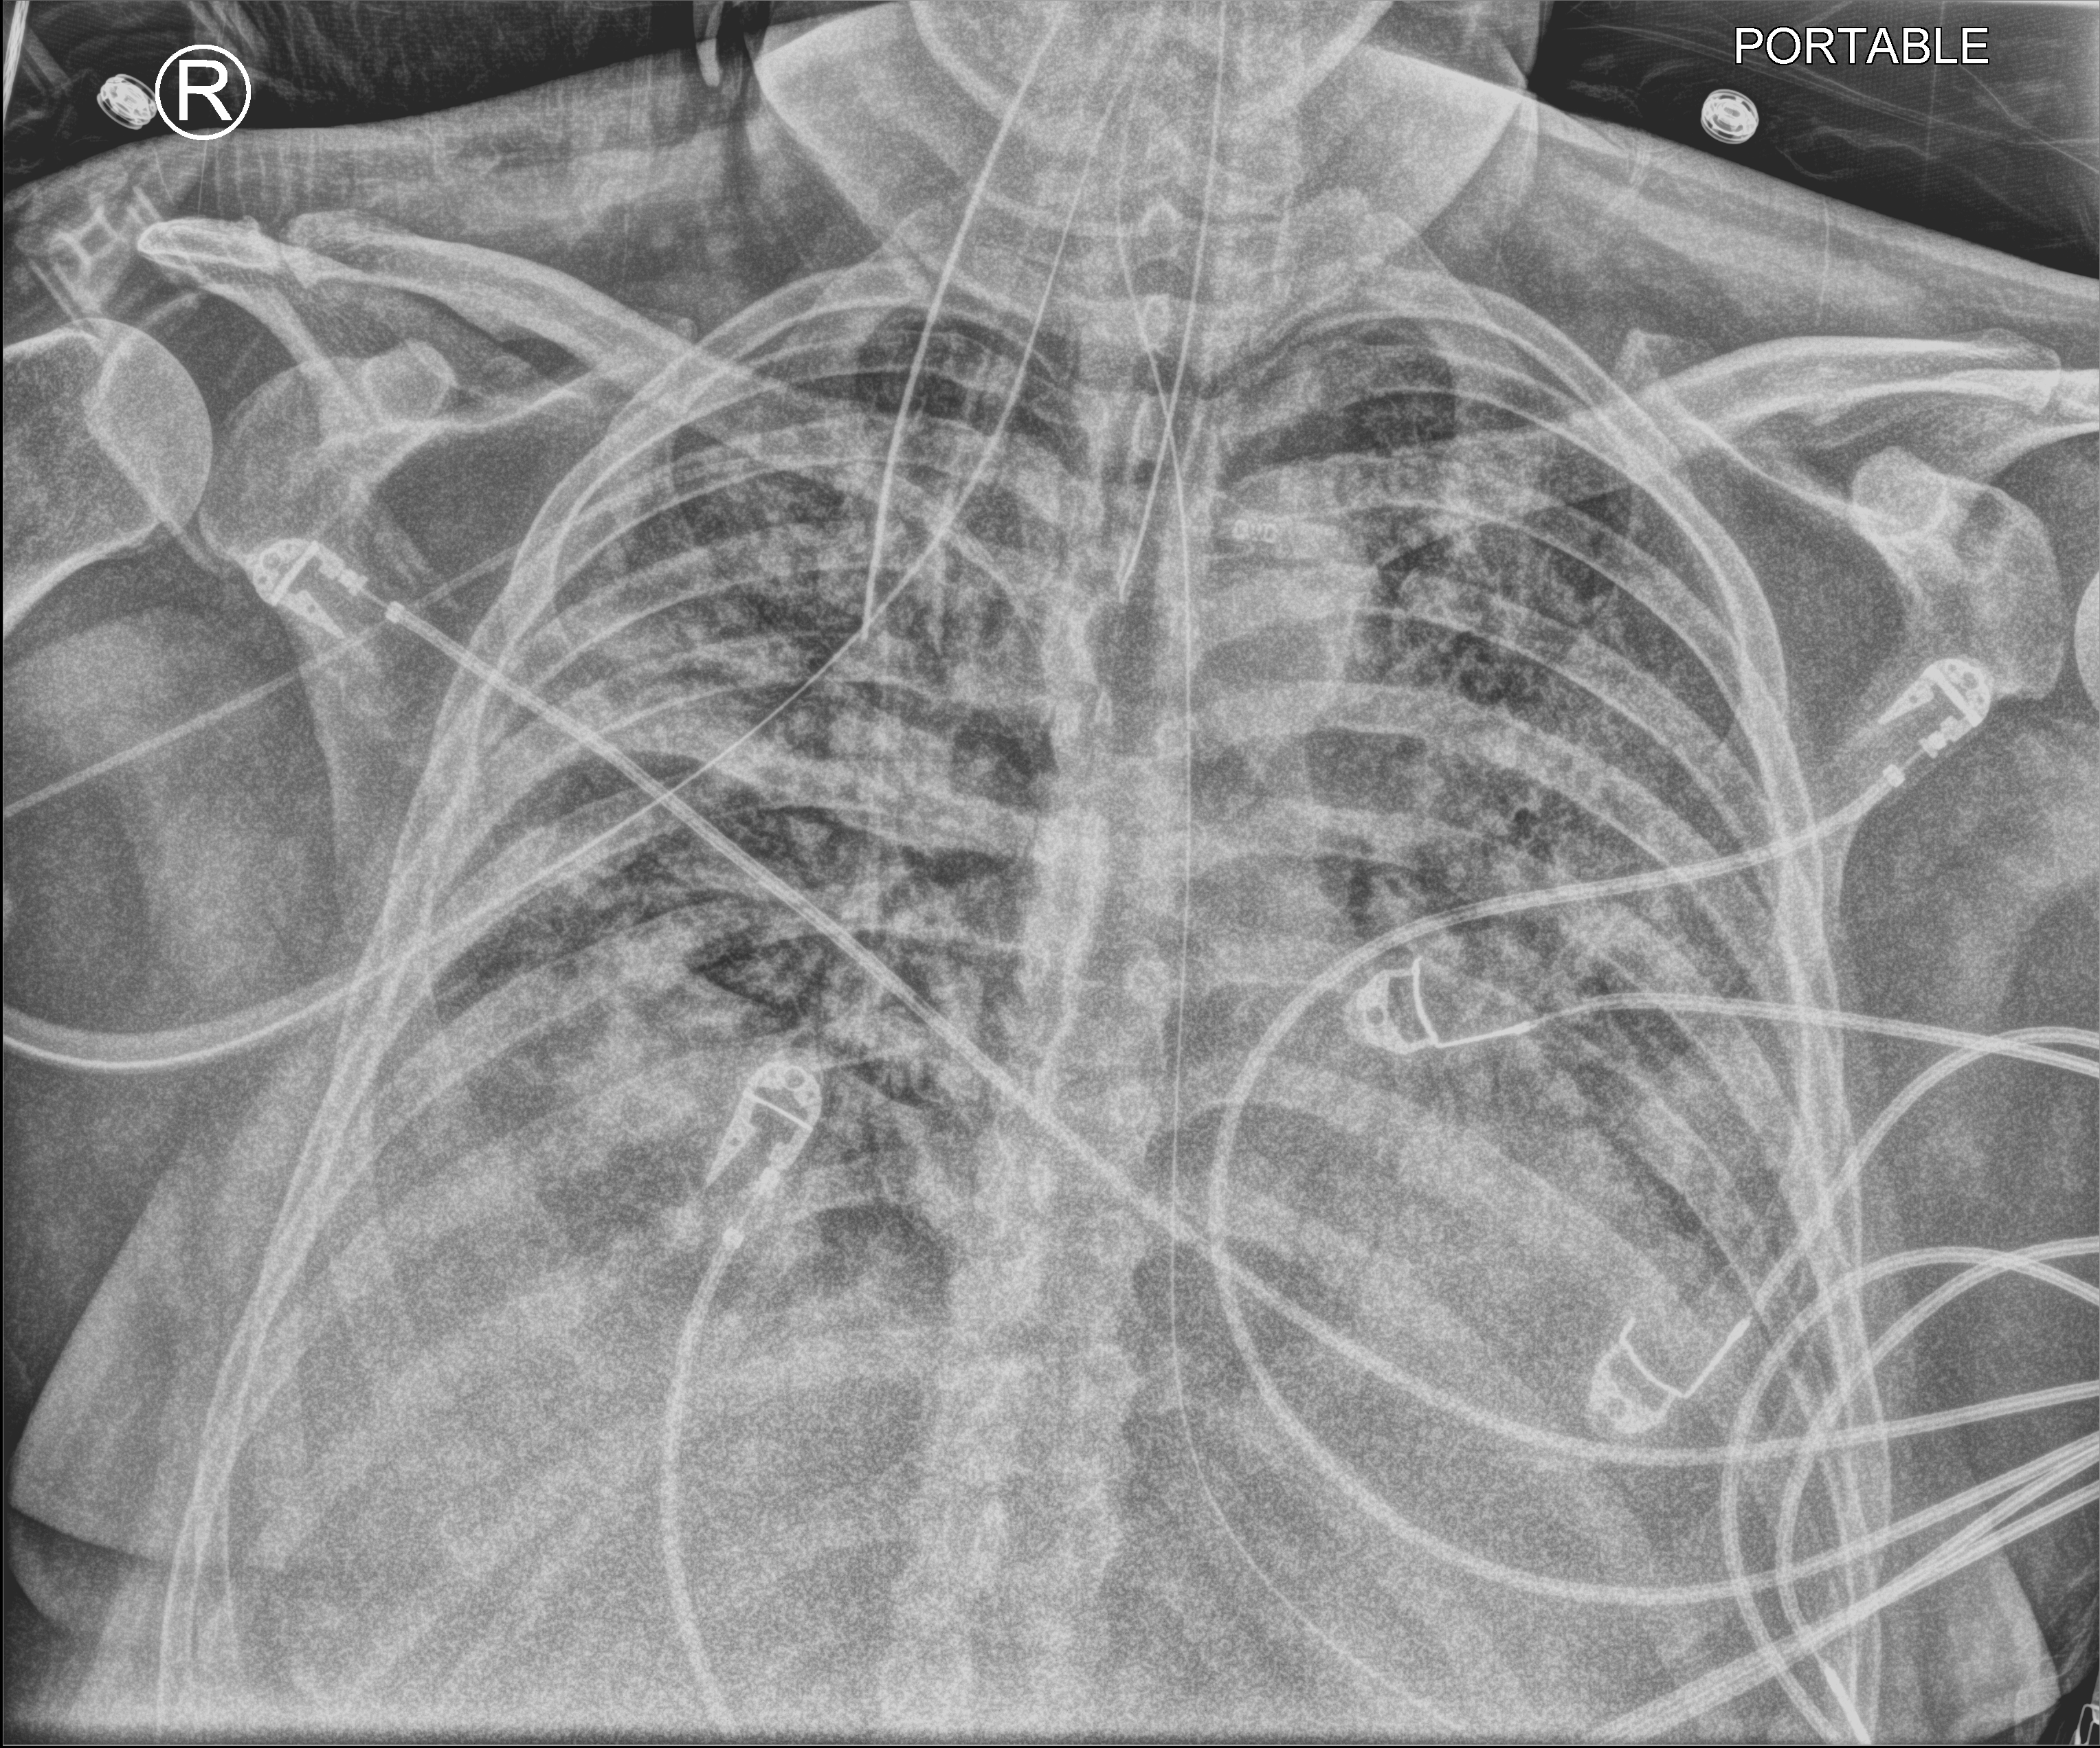
Chest X-ray (portable), anteroposterior (AP) projection. Patient hospitalised with COVID-19; male, aged 18–59 years.
From the hospital-stay record, not from the radiograph (when in the stay this image was taken is not recorded): mechanically ventilated during this hospital stay: yes; admitted to intensive care during this hospital stay: yes.